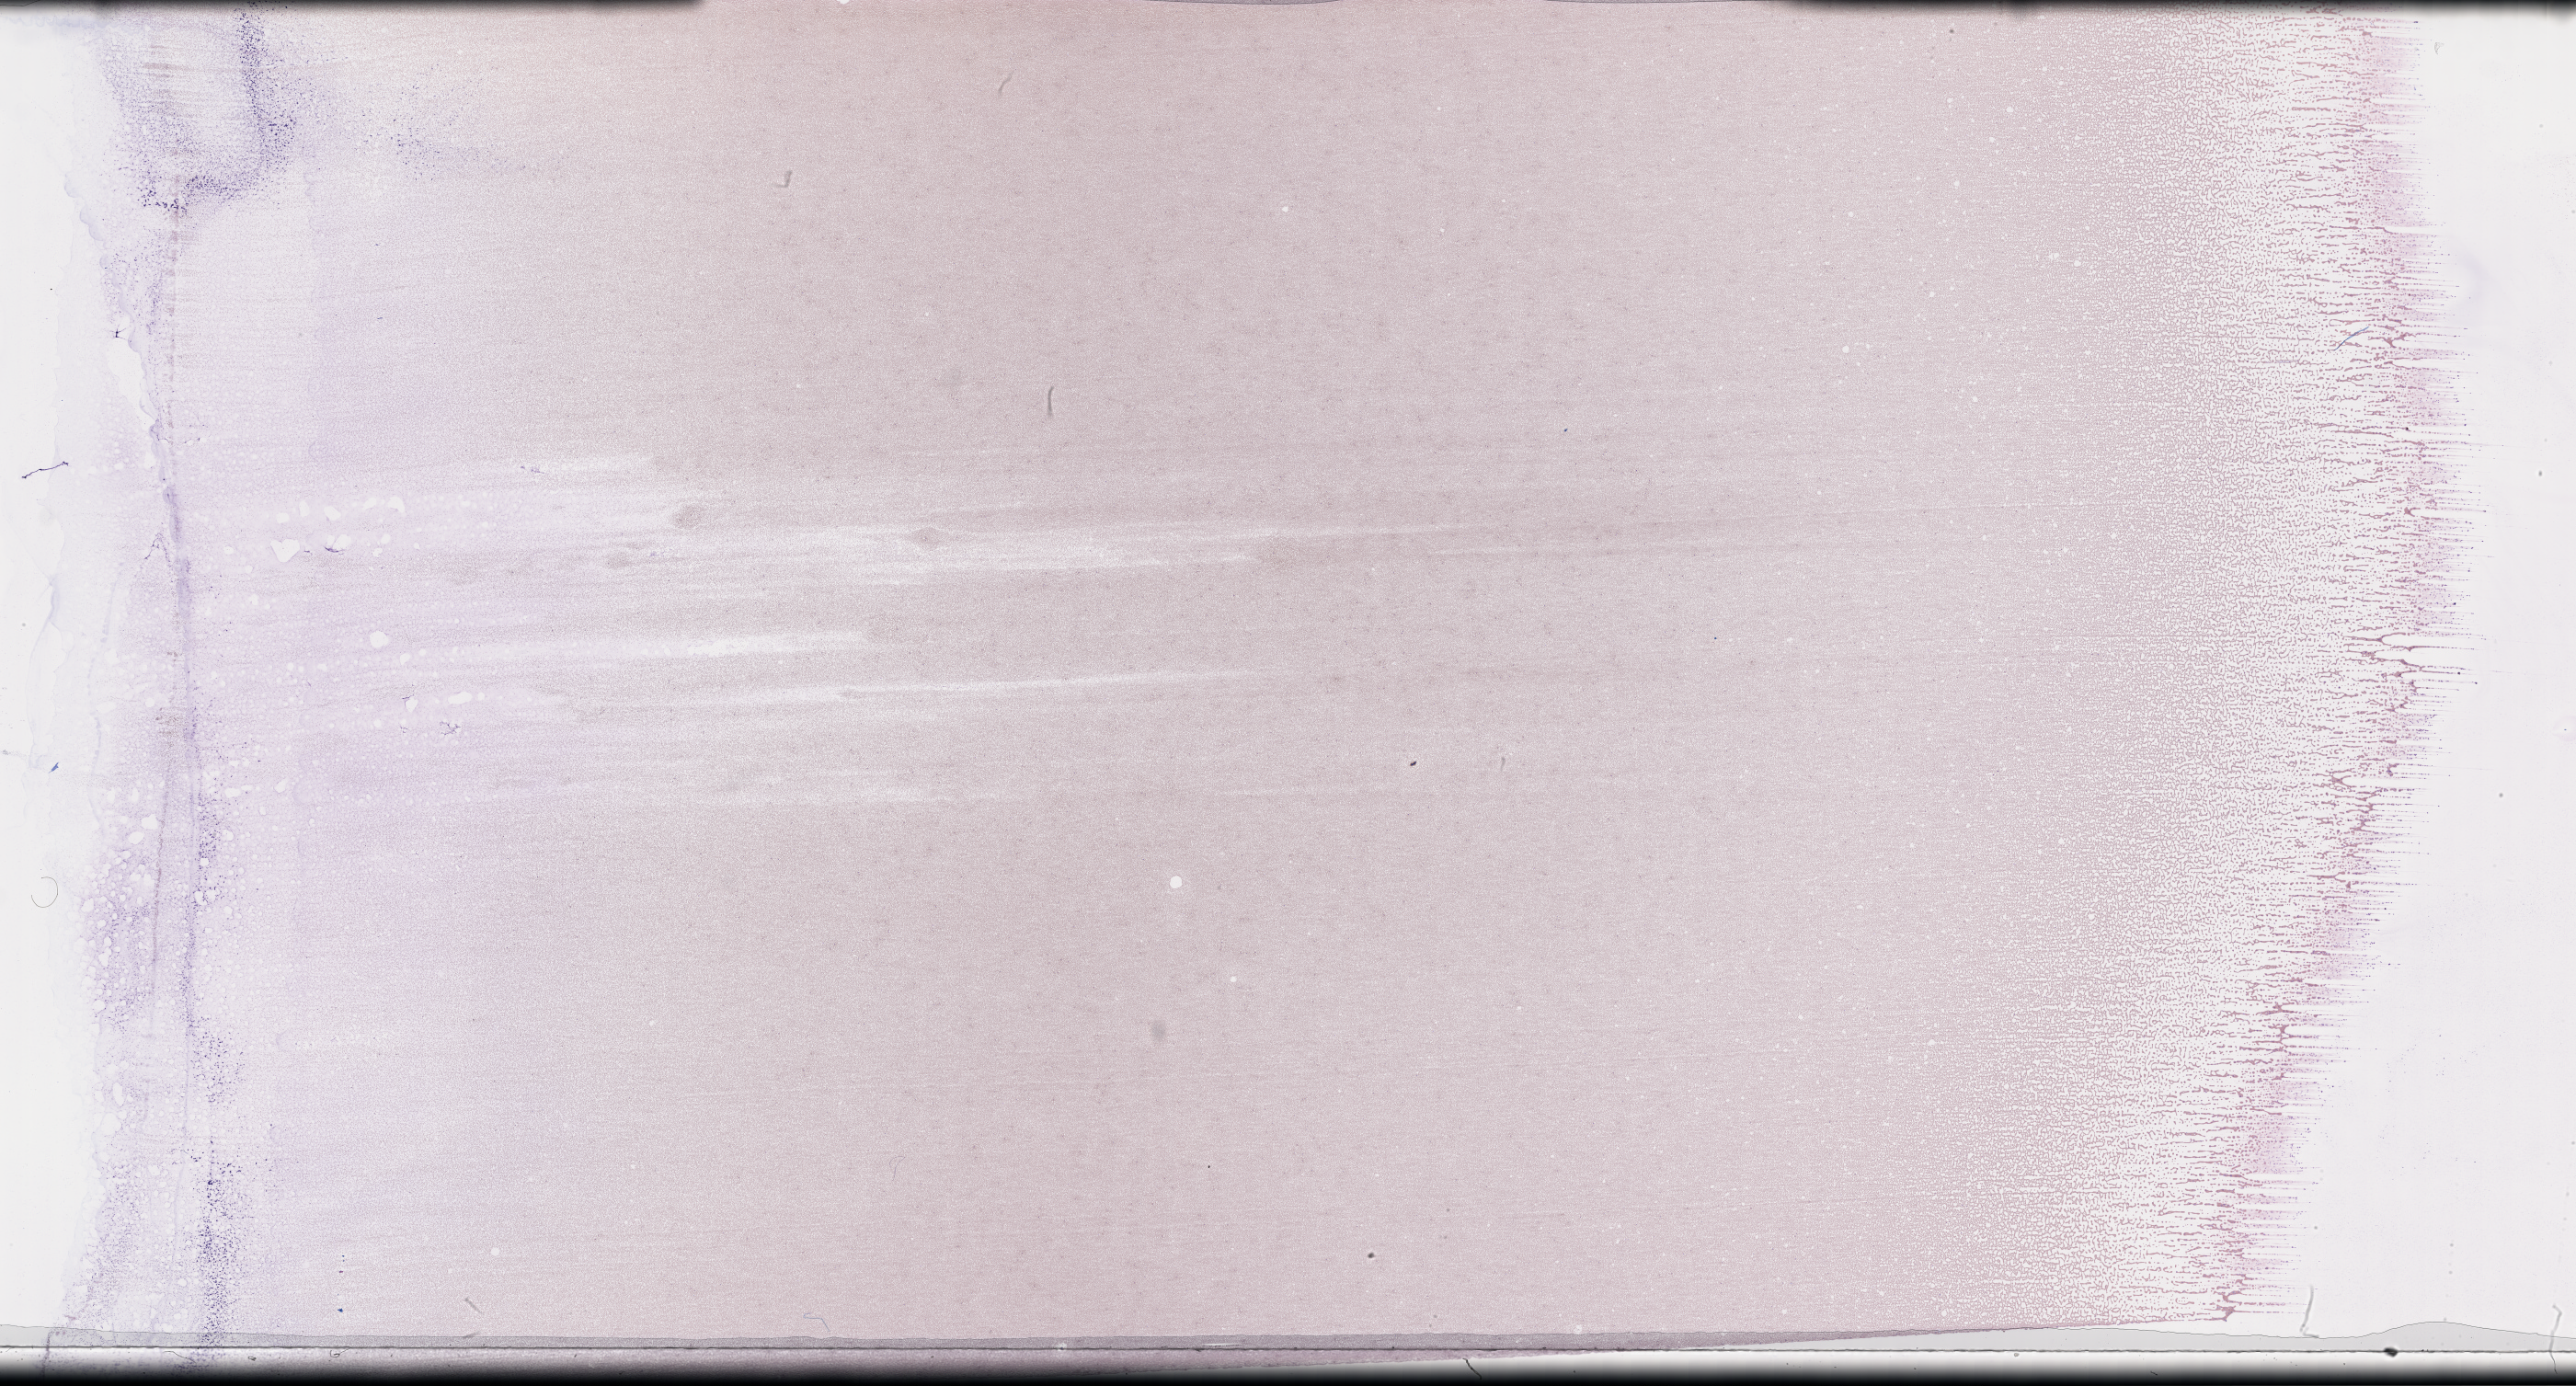
Whole-slide image of a whole blood smear, Wright-Giemsa stain — low-resolution overview of the scanned area, about 45.2 x 24.3 mm, smear from an EDTA sample, specimen time point: collected on treatment. Patient sex: female.
From a patient with: Plasma Cell Myeloma.